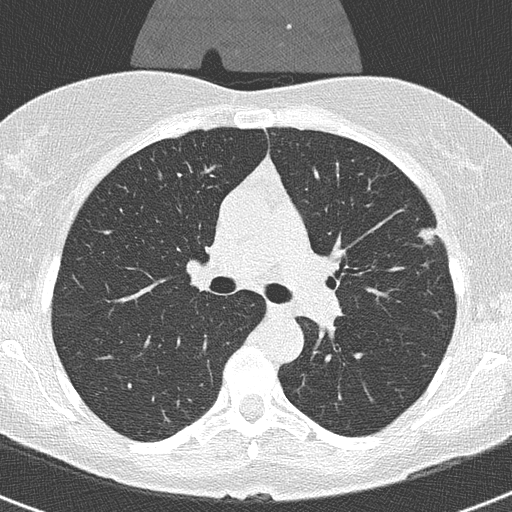
Chest CT (low-dose screening protocol), one axial image; second screening round (one year after baseline); lung window (W 1500 / L -600 HU); 2 mm slice thickness; slice 110 of 320 in the series; 512 × 512 image matrix, field of view 290 × 290 mm. Female participant, aged 56 years at enrolment. Former smoker at enrolment.
Expert reader's lesion annotation, bounding box (x1, y1, x2, y2) in pixels: (403, 201, 453, 256). Screening reader's record for this exam (one nodule recorded; not confirmed to be the boxed lesion): non-calcified nodule or mass ≥4 mm, left upper lobe, 20 × 9 mm, smooth margins, soft tissue attenuation, pre-existing on the prior screen: yes; interval growth: yes. Participant outcome: lung cancer diagnosed 55 days after this screen — adenocarcinoma, NOS, left upper lobe, moderately differentiated (G2), stage IA (AJCC 6th edition), 11 mm at pathology.